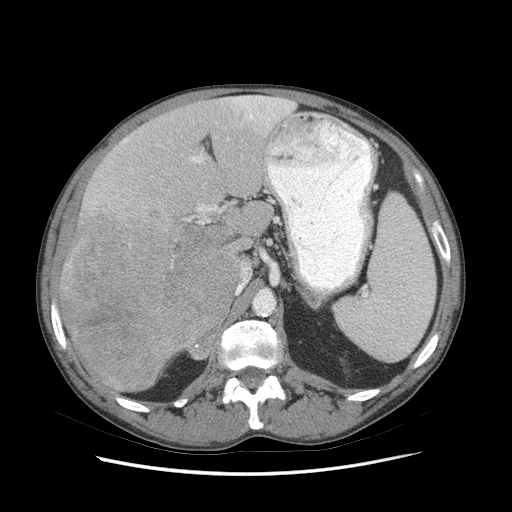
Contrast-enhanced abdominal CT (liver protocol), one axial slice; position 47 of 89 along the scan axis; 140 kVp; soft-tissue window (W 400 / L 40 HU); 2.5 mm slice thickness; 512 × 512 image matrix. From the clinical record (not read from this slice): diagnosis: hepatocellular carcinoma (patient treated with transarterial chemoembolisation; whether this scan precedes or follows treatment is not stated here); TNM stage (as recorded): Stage-IIIB; Child-Pugh class: A; tumour differentiation: moderately differentiated; tumour nodularity: multinodular.
Outlined on this slice (semi-automatically segmented with operator editing):
- liver parenchyma outside the tumour (the mass and vessels are separate outlines, so this box may not span the whole liver): bounding box [x1, y1, x2, y2] px = [58, 96, 294, 392]
- mass: [57, 206, 241, 391]
- liver vessels: [94, 96, 293, 223]